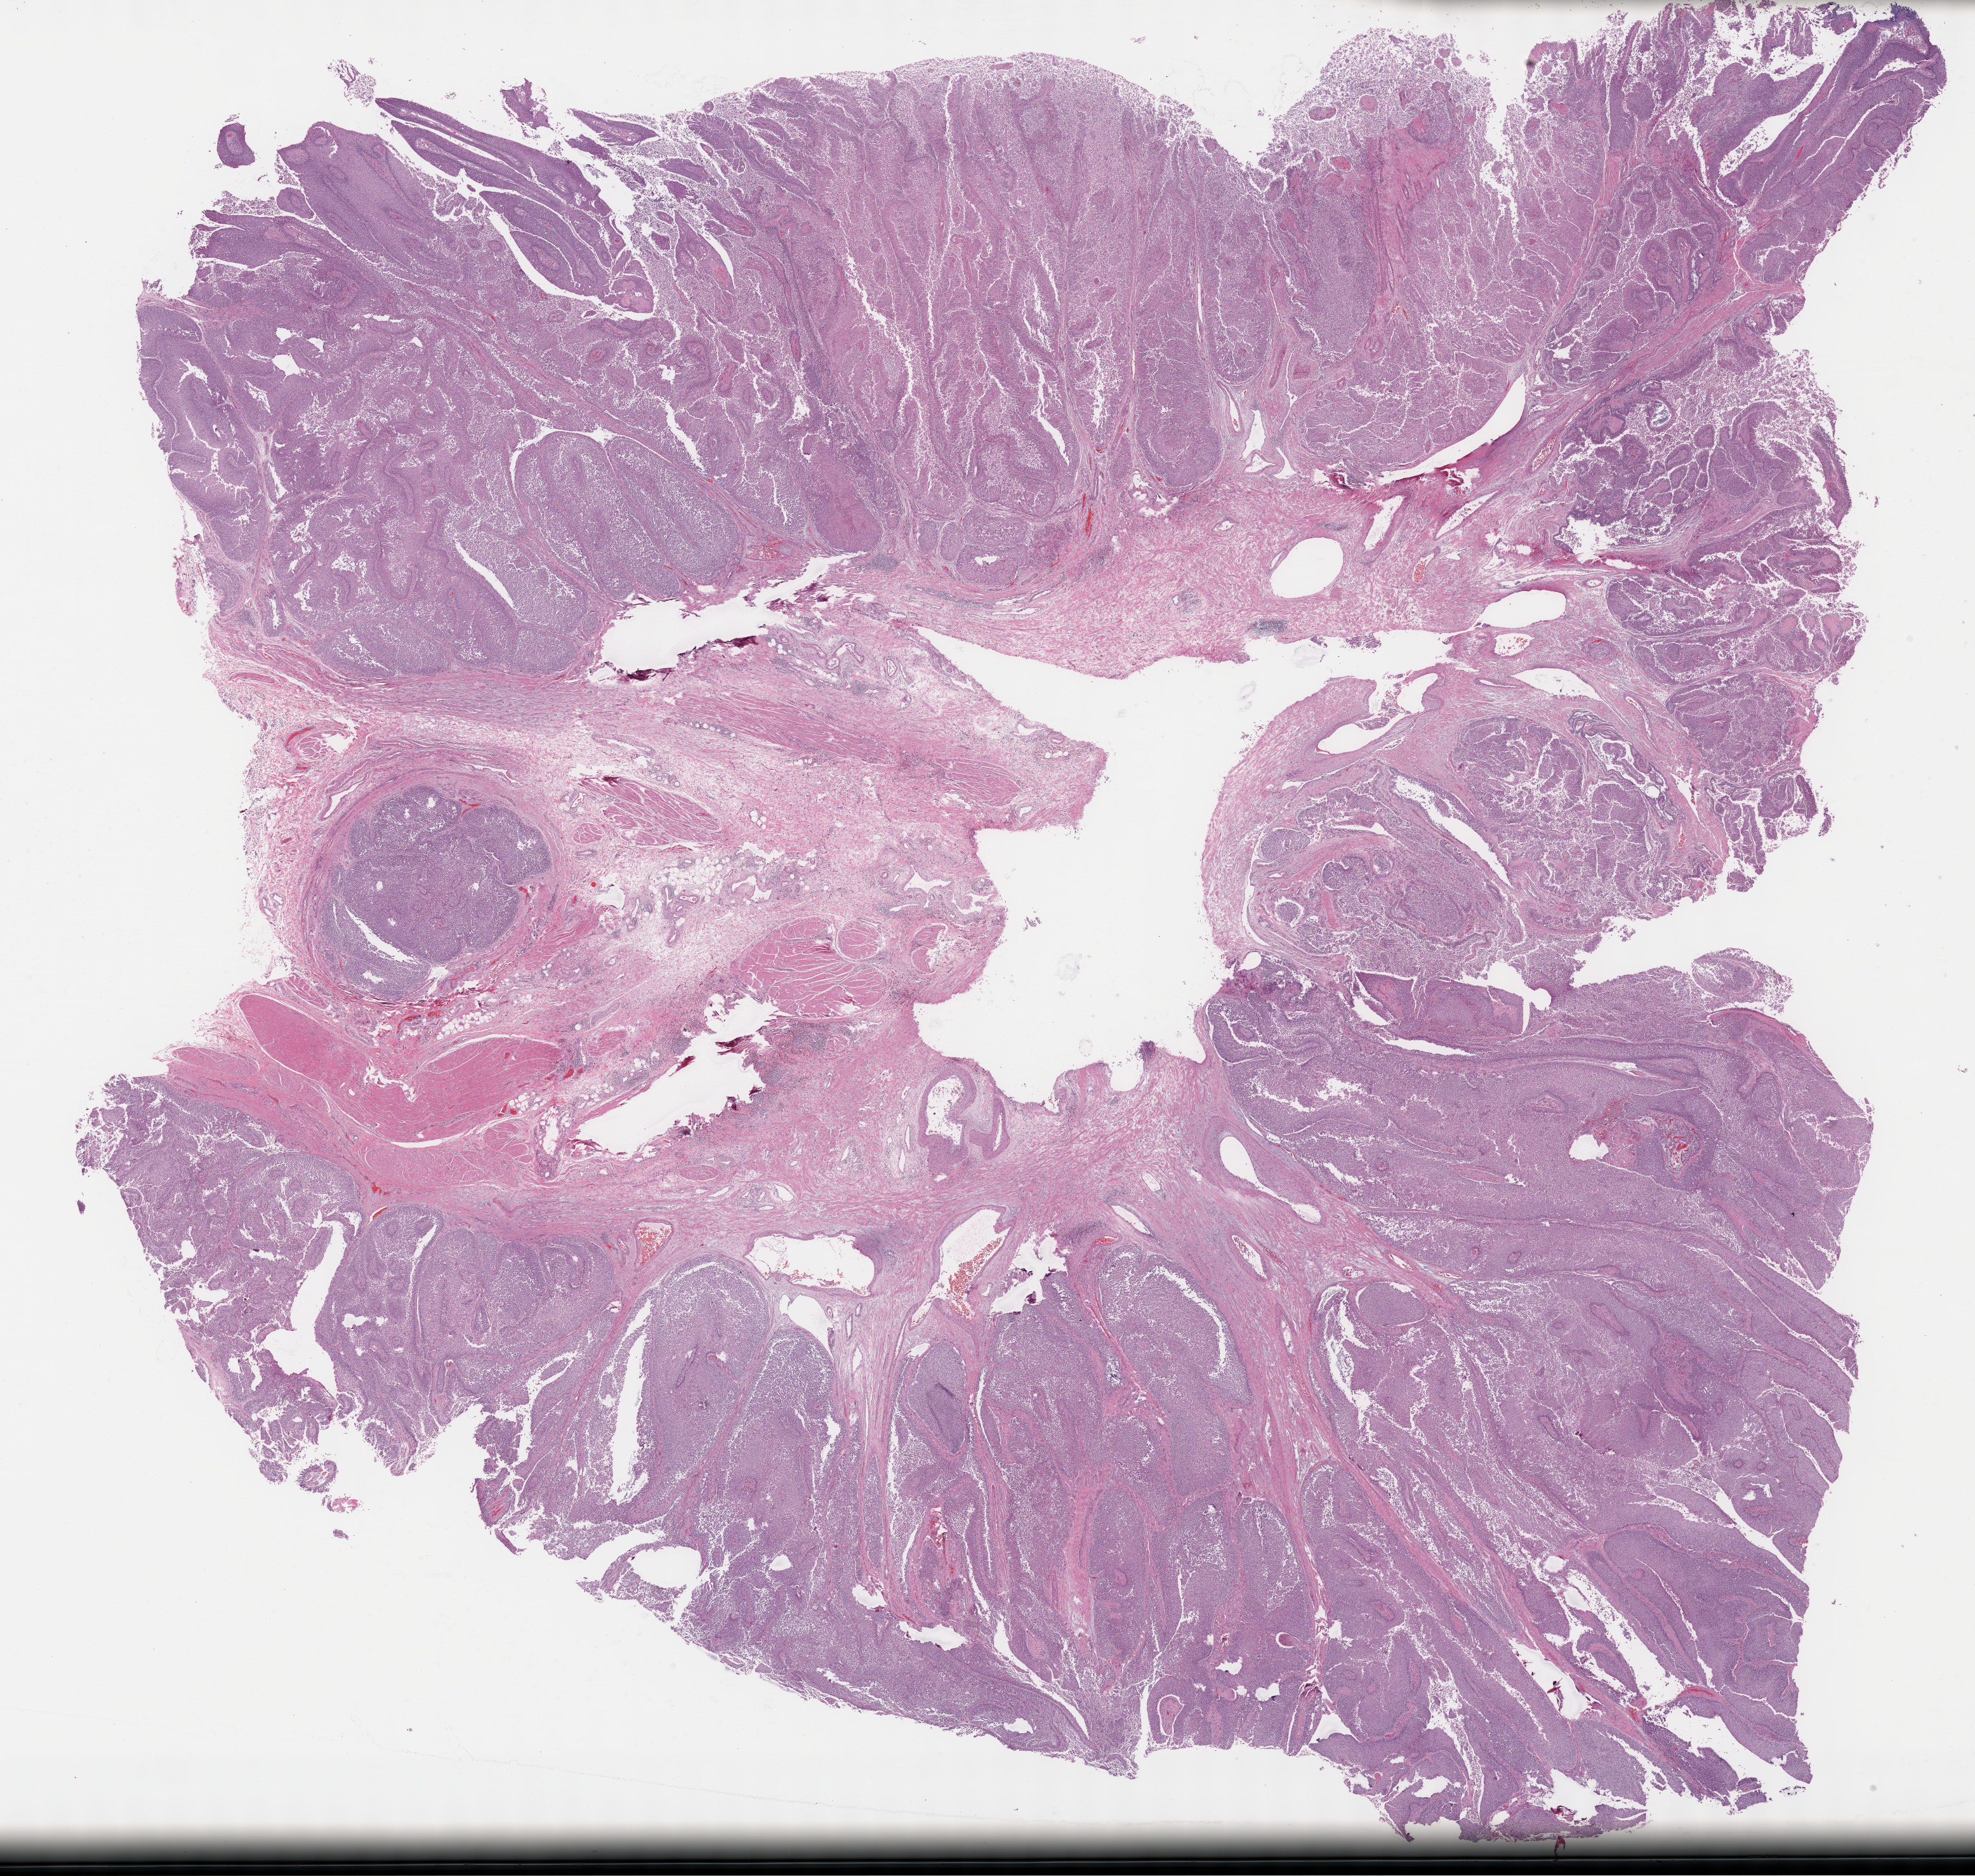
Whole-slide histology image, H&E, a low-resolution overview of the entire scanned area, about 25.2 x 23.9 mm (from a 40x scan), formalin-fixed paraffin-embedded (FFPE) diagnostic section, primary tumour sample from the bladder. Patient: male, age at initial diagnosis 57 years. Histologic grade: high grade.
Lymph nodes positive (case pathology): 0 of 13 examined. Diagnosis: Transitional cell carcinoma. AJCC pathologic stage: III (6th edition).